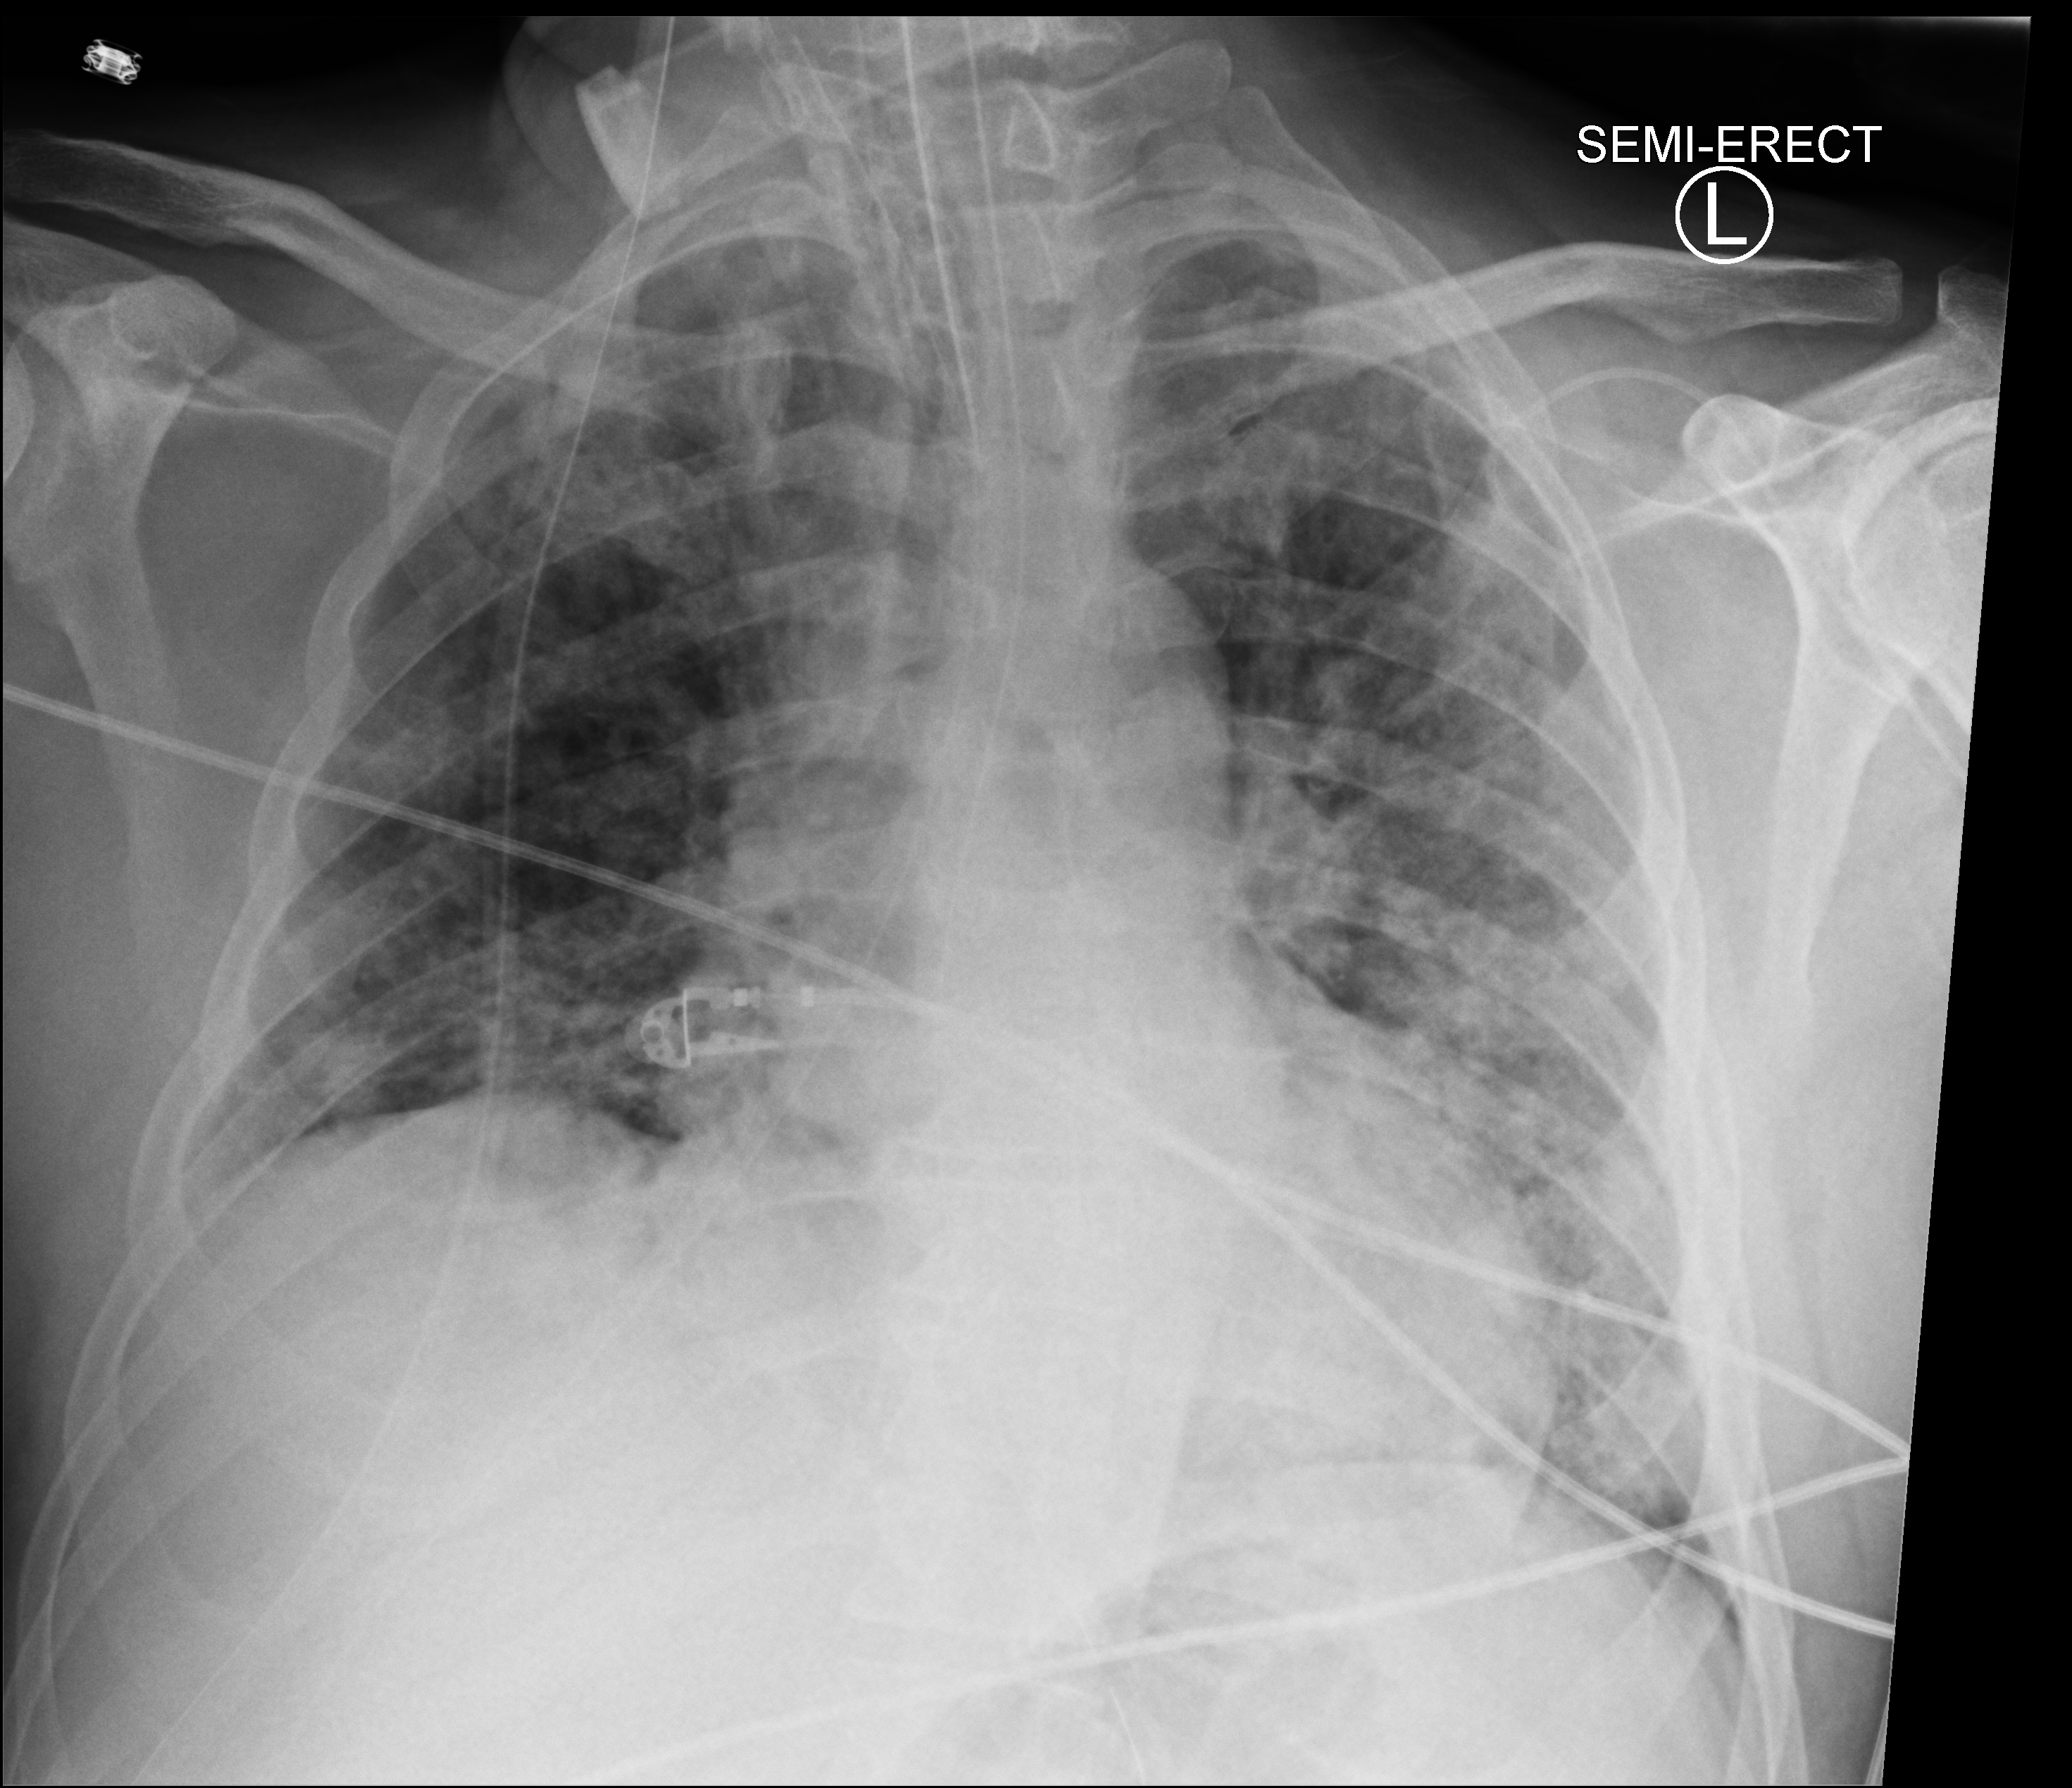
Chest X-ray (portable); anteroposterior (AP) projection. Male patient hospitalised with COVID-19, age 18–59 years.
Admission-level facts for this patient (not findings on this image; timing relative to this image not recorded): length of hospital stay: 32 days; mechanically ventilated during this hospital stay: yes.